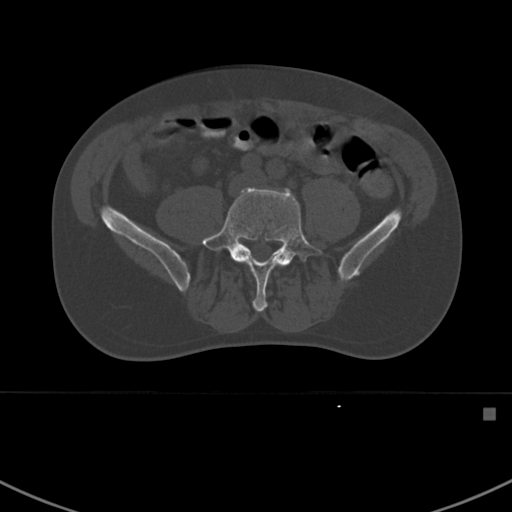
CT including the spine, one axial slice; position 222 of 412 along the scan axis; reconstruction kernel Br40s; 120 kVp; bone window (W 1800 / L 400 HU); 1.5 mm slice thickness; 512 × 512 image matrix, field of view 358 × 358 mm. Patient: male, 59 years. Case-level facts recorded for this patient, not image findings: primary cancer: prostate.
Annotated regions visible in this slice (semi-automatically segmented with operator editing):
- L5 vertebra: bounding box <201,188,323,312> (left, top, right, bottom; pixels)